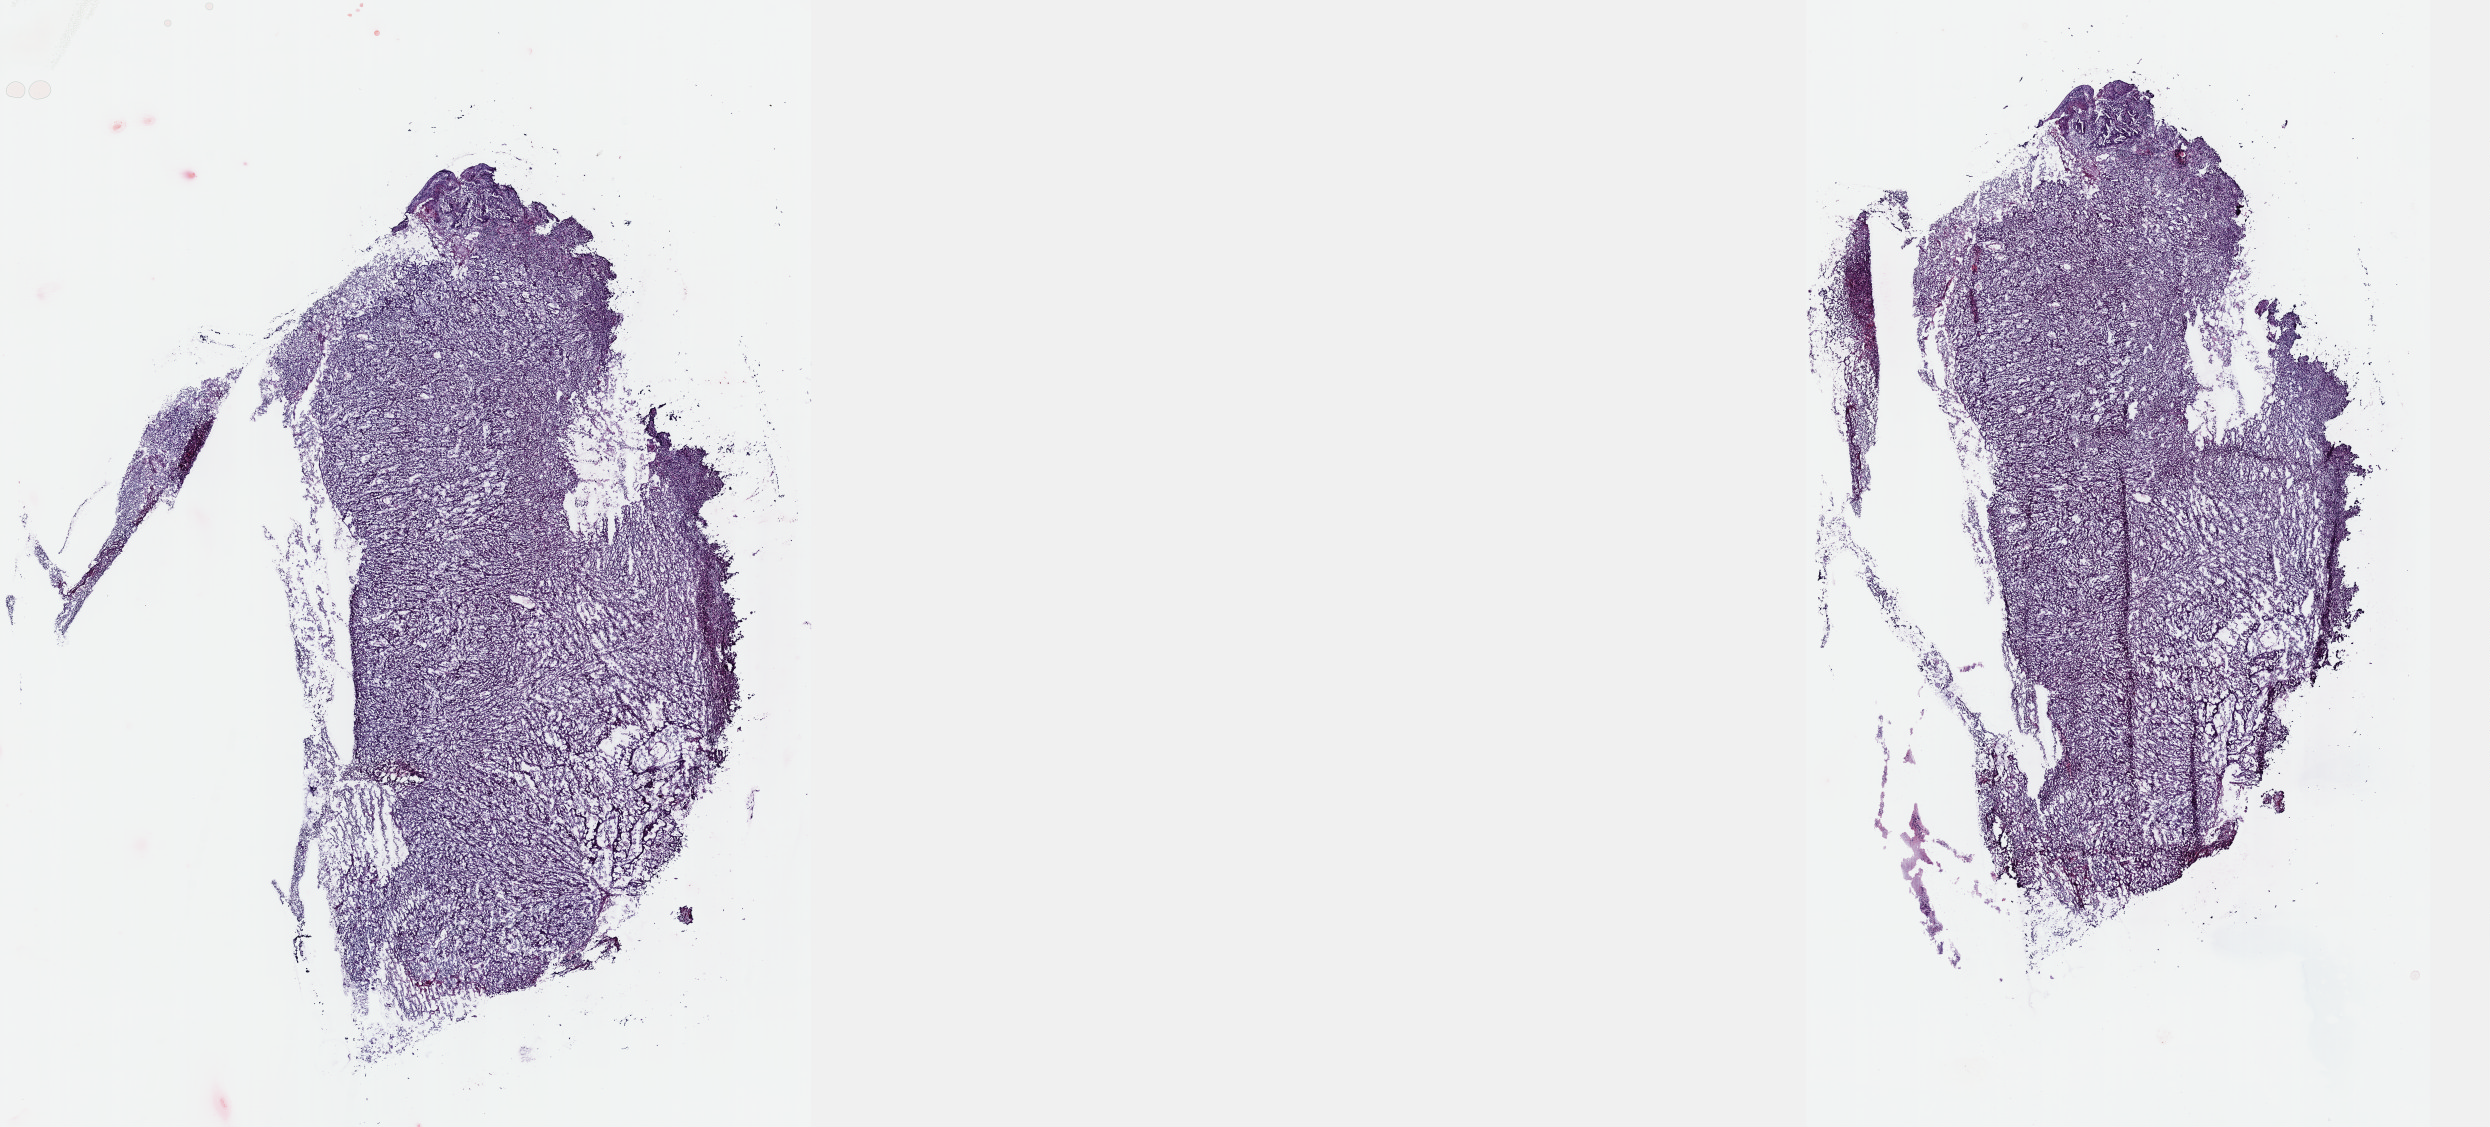
Digitized H&E-stained tissue section (whole slide), a low-resolution overview of the entire scanned area, about 20.1 x 9.1 mm, frozen section from the top of the tissue portion, sample: primary tumour, stomach. Female patient; age at initial diagnosis 78 years. Histologic grade: G3 (poorly differentiated). Pathologist review of this section (percent, as recorded): tumour cells 100%, tumour nuclei 75%, normal cells 0%, stromal cells 0%, necrosis 0%. Infiltration values recorded for this section: lymphocyte infiltration 3%, monocyte infiltration 0%, neutrophil infiltration 0%.
Lymph nodes positive (case pathology): 0 of 42 examined. Histologic diagnosis: Adenocarcinoma, NOS (cardia, NOS). AJCC pathologic stage: IIA. TNM: T3 N0 M0.